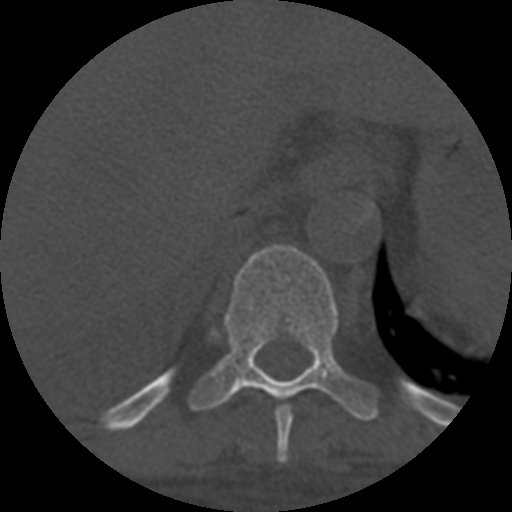
CT including the spine, one axial slice; slice 361 of 708 in the series (ordered by position); 120 kVp; one of 3 acquisitions stored at this slice position; bone window (W 1800 / L 400 HU); 1.25 mm slice thickness; 512 × 512 image matrix, field of view 160 × 160 mm. Patient age 55 years. From the clinical record (not read from this slice): primary cancer: colon; vertebrae with lytic lesions (as recorded): T12, L1, L5.
Annotated regions visible in this slice (semi-automatic segmentation, software-assisted and operator-edited):
- T10 vertebra: bounding box (x1, y1, x2, y2) in pixels: (188, 244, 379, 421)
- T9 vertebra: (275, 405, 293, 463)